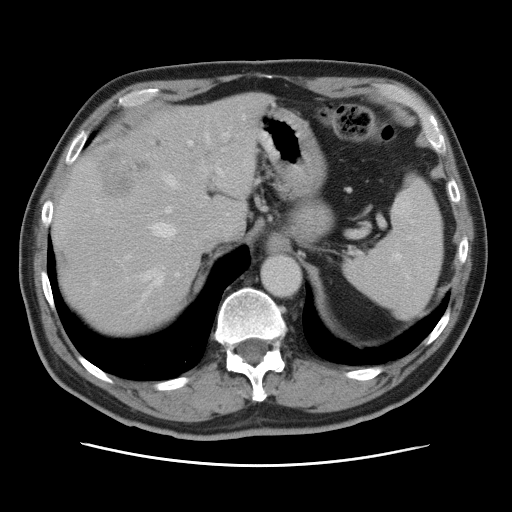
Contrast-enhanced abdominal CT, one axial slice. Position 59 of 80 along the scan axis. Soft-tissue window (W 400 / L 40 HU). 5 mm slice thickness. 512 × 512 image matrix. Male patient, age 69 years. Case-level facts recorded for this patient, not image findings: diagnosis: colorectal cancer liver metastases, imaged before liver resection; multiple liver metastases: no; largest metastasis: 5 cm.
Annotated regions visible in this slice (outlined manually by an expert reader):
- hepatic veins: bounding box [x1, y1, x2, y2] px = [141, 132, 210, 298]
- liver: [55, 94, 266, 333]
- planned liver remnant (the part of the liver to remain after resection): [54, 94, 265, 333]
- portal vein (with intrahepatic branches): [124, 126, 233, 276]
- liver metastasis: [94, 148, 149, 197]